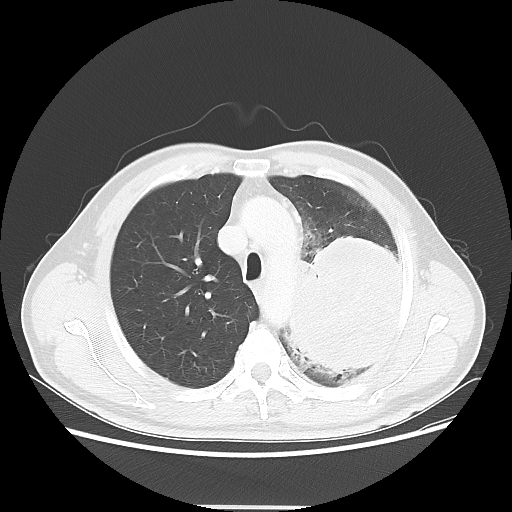
Chest CT, one axial slice. Slice 40 of 53 in the series (ordered by position). Reconstruction kernel LUNG. Lung window (W 1500 / L -600 HU). 5 mm slice thickness. 512 × 512 image matrix, field of view 391 × 391 mm. Patient: male, 60 years. From the clinical record (not read from this slice): clinical TNM (as recorded): T4 N1 M1a; histopathological grade: G3.
Outlined on this slice (bounding box drawn by a radiologist):
- lung tumour (recorded histology: large cell carcinoma): box from (x=283, y=220) to (x=407, y=379) px